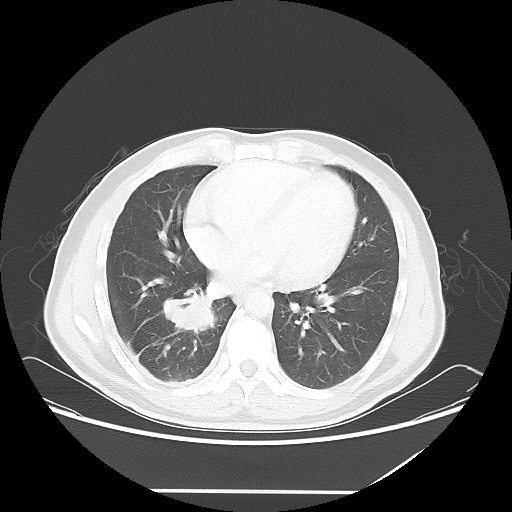
Chest CT, one axial slice; position 25 of 60 along the scan axis; reconstruction kernel LUNG; 120 kVp; lung window (W 1500 / L -600 HU); 5 mm slice thickness; 512 × 512 image matrix, field of view 419 × 419 mm. Patient: male, 48 years. From the clinical record (not read from this slice): clinical TNM (as recorded): T3 N3 M1a.
Outlined on this slice (rectangle marked by the reading radiologist):
- lung tumour (recorded histology: squamous cell carcinoma): bounding box <155,285,219,339> (left, top, right, bottom; pixels)